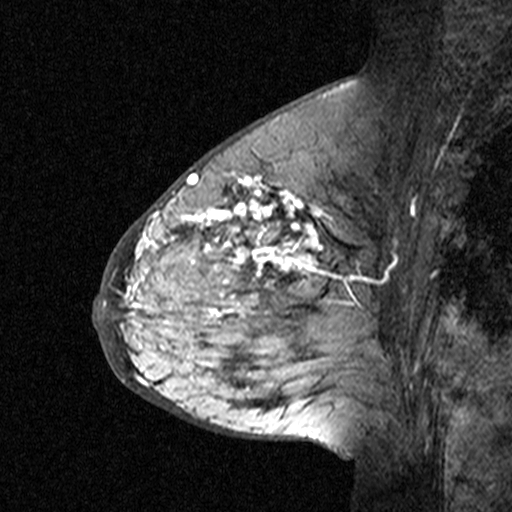
Breast MRI (dynamic contrast-enhanced), one sagittal slice. Position 19 of 44 along the scan axis. Dynamic contrast-enhanced study with each time point stored as its own series, time point 3 of 4 at this slice position (ordered by acquisition time). 1.5 T. TE 4.5 ms, TR 11 ms. 512 × 512 image matrix, field of view 200 × 200 mm. Female patient, age 65 years. From the clinical record (not read from this slice): setting: breast cancer imaged before/during neoadjuvant chemotherapy; receptor status: HER2-positive.
Structures marked on this image (semi-automatically segmented with operator editing):
- analysis volume of interest (the breast-tissue region the enhancement analysis was run in; not a lesion): box from (x=182, y=190) to (x=353, y=361) px
- tumour enhancement mask (voxels above the 90 % enhancement threshold inside the analysis volume of interest): (x=188, y=190)–(x=319, y=315)